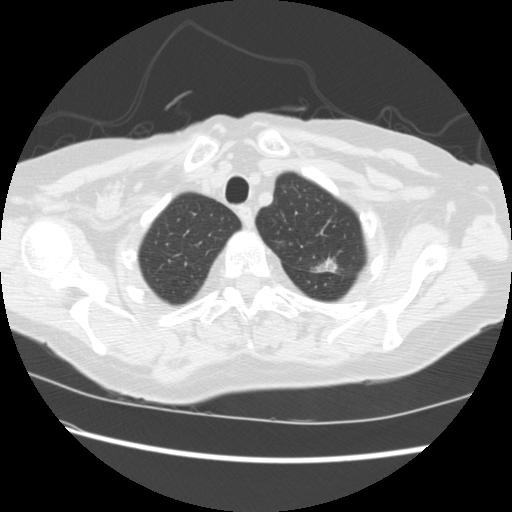
Low-dose screening chest CT, one axial slice; slice 190 of 224 in the series (ordered by position); reconstruction kernel STANDARD; lung window (W 1500 / L -600 HU); 512 × 512 image matrix, field of view 340 × 340 mm.
Outlined on this slice (expert manual segmentation):
- lesion 1 (tumor, upper lobe of left lung): bounding box [x1, y1, x2, y2] px = [315, 259, 337, 272]